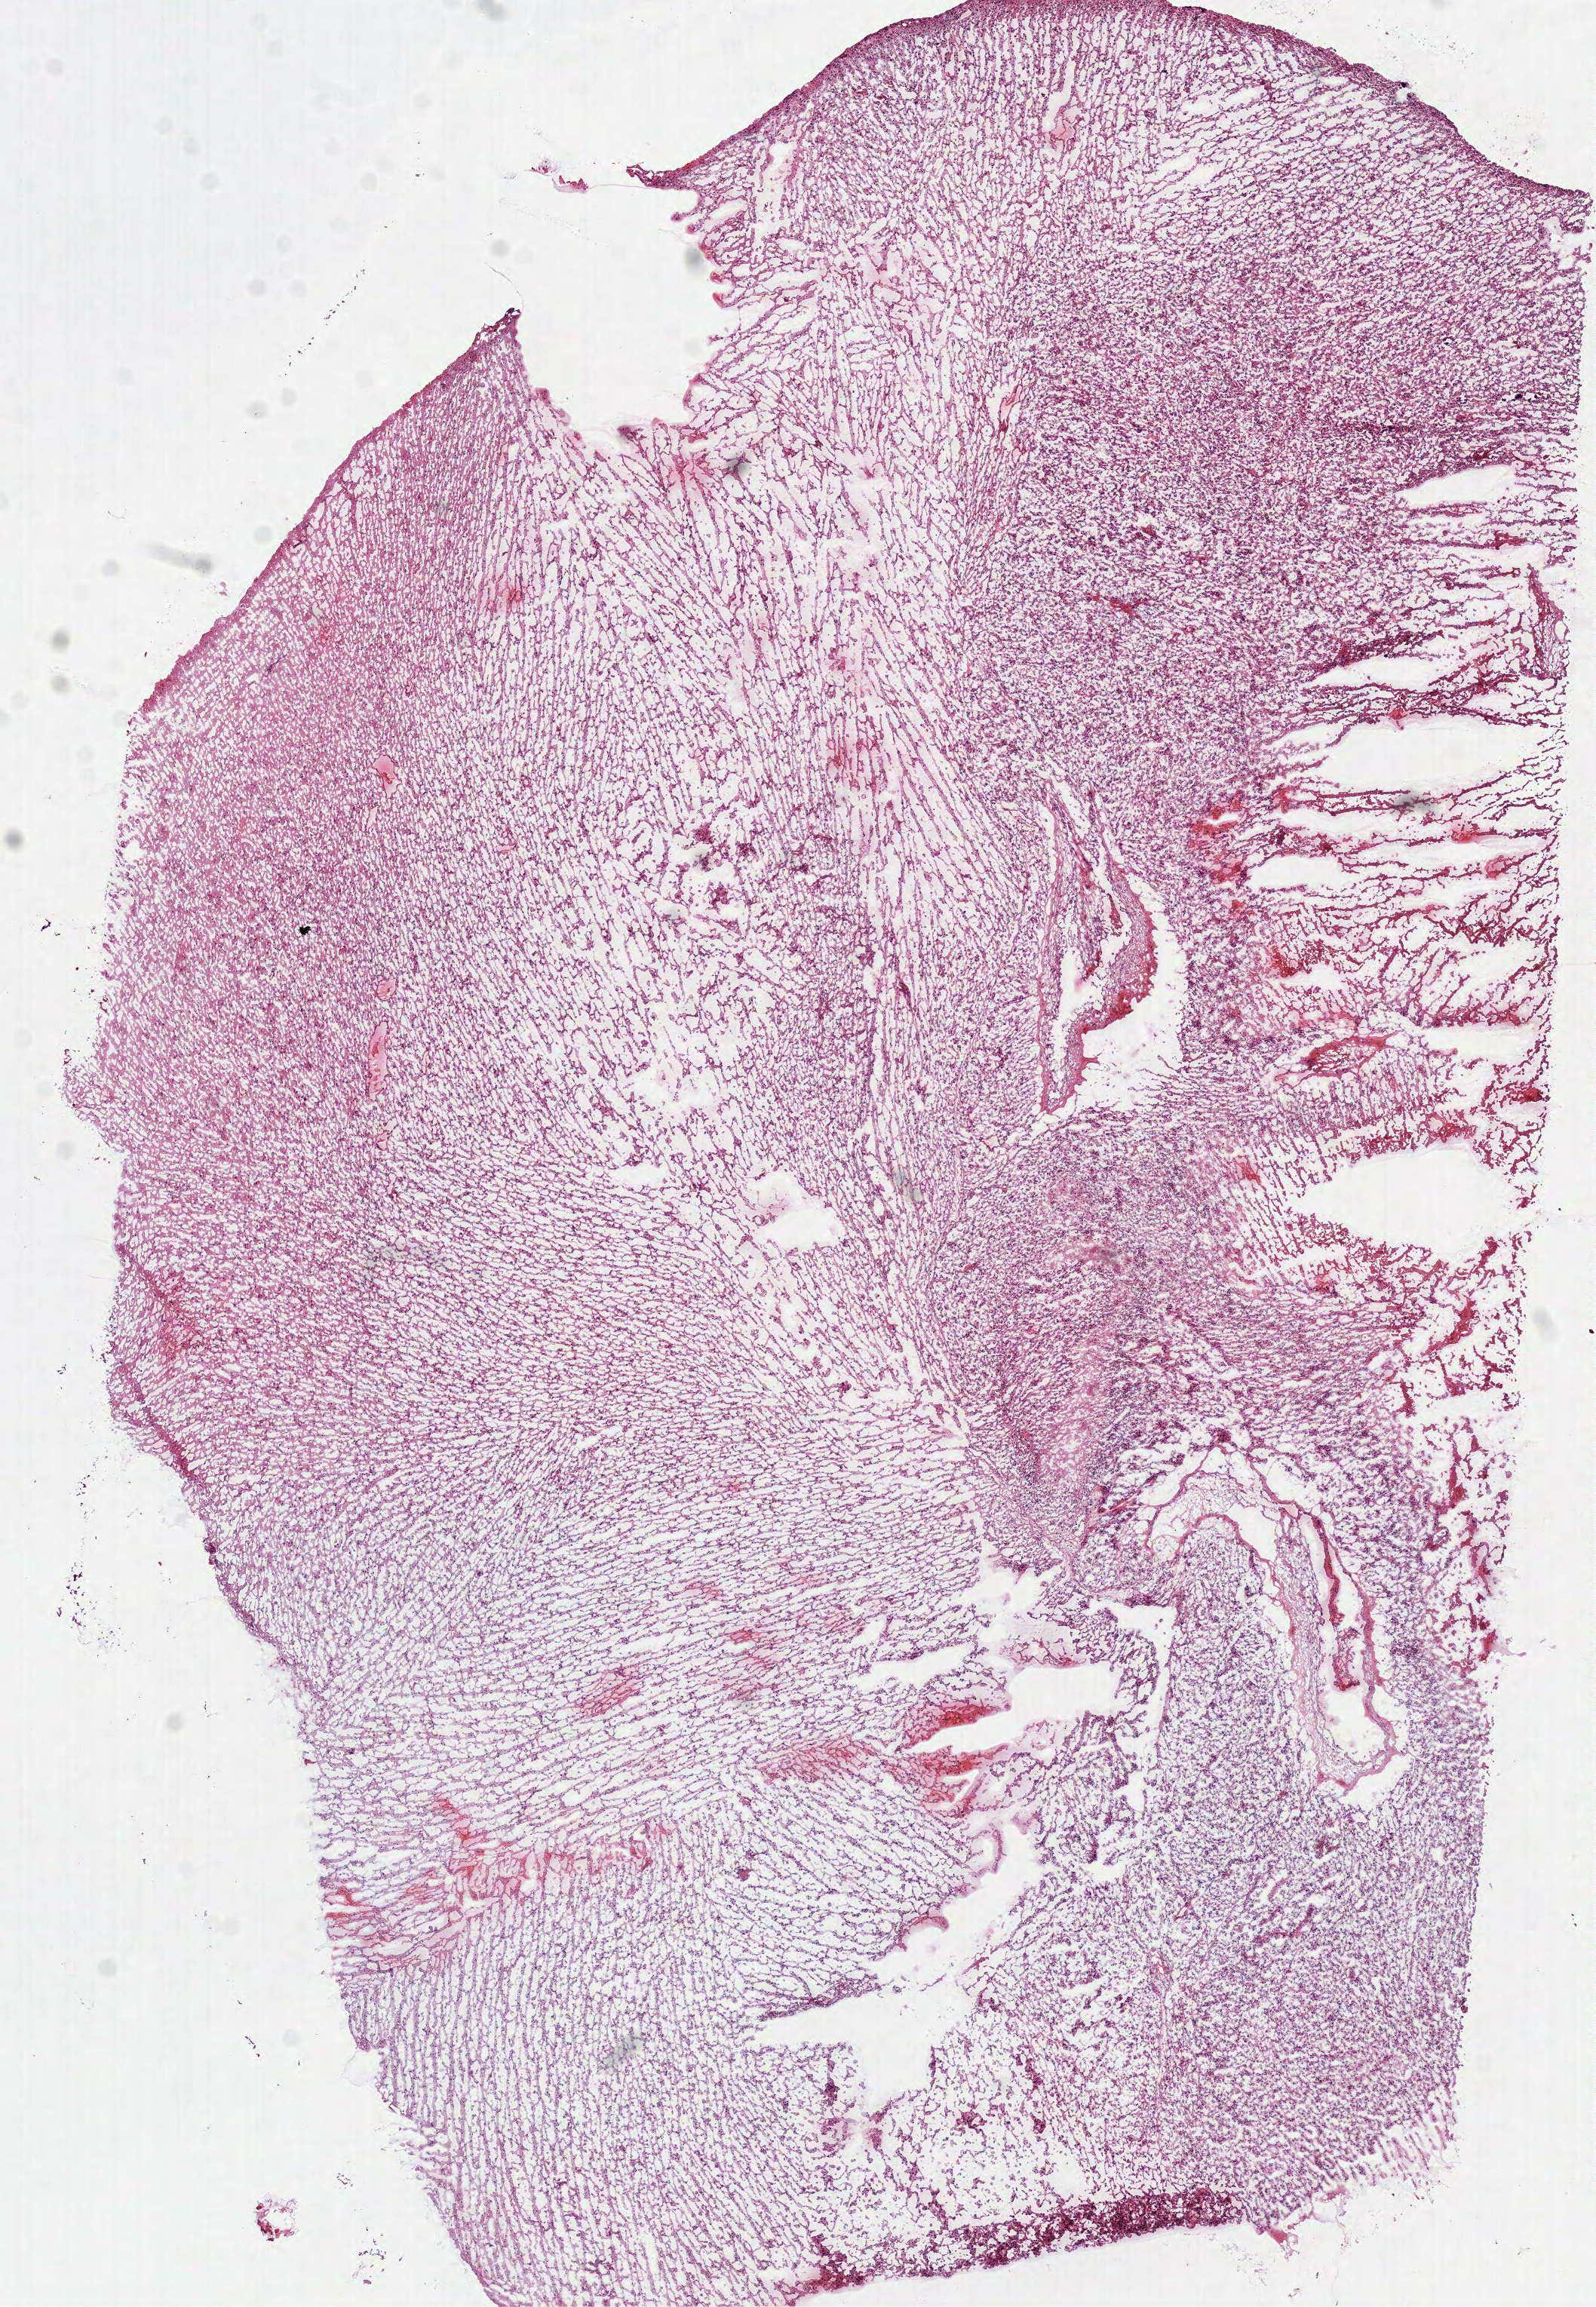
Digitized H&E tissue section (whole slide) — whole scanned area (about 8.5 x 12.3 mm, slide scanned at 40x) shown as a low-resolution overview, frozen section, primary tumour sample from the brain. Patient: male, age at initial diagnosis 54 years. Pathologist review of this section (percent, as recorded): tumour cells 90%, tumour nuclei 75%, normal cells 0%, stromal cells 0%, necrosis 10%.
Pathologic diagnosis: Glioblastoma.